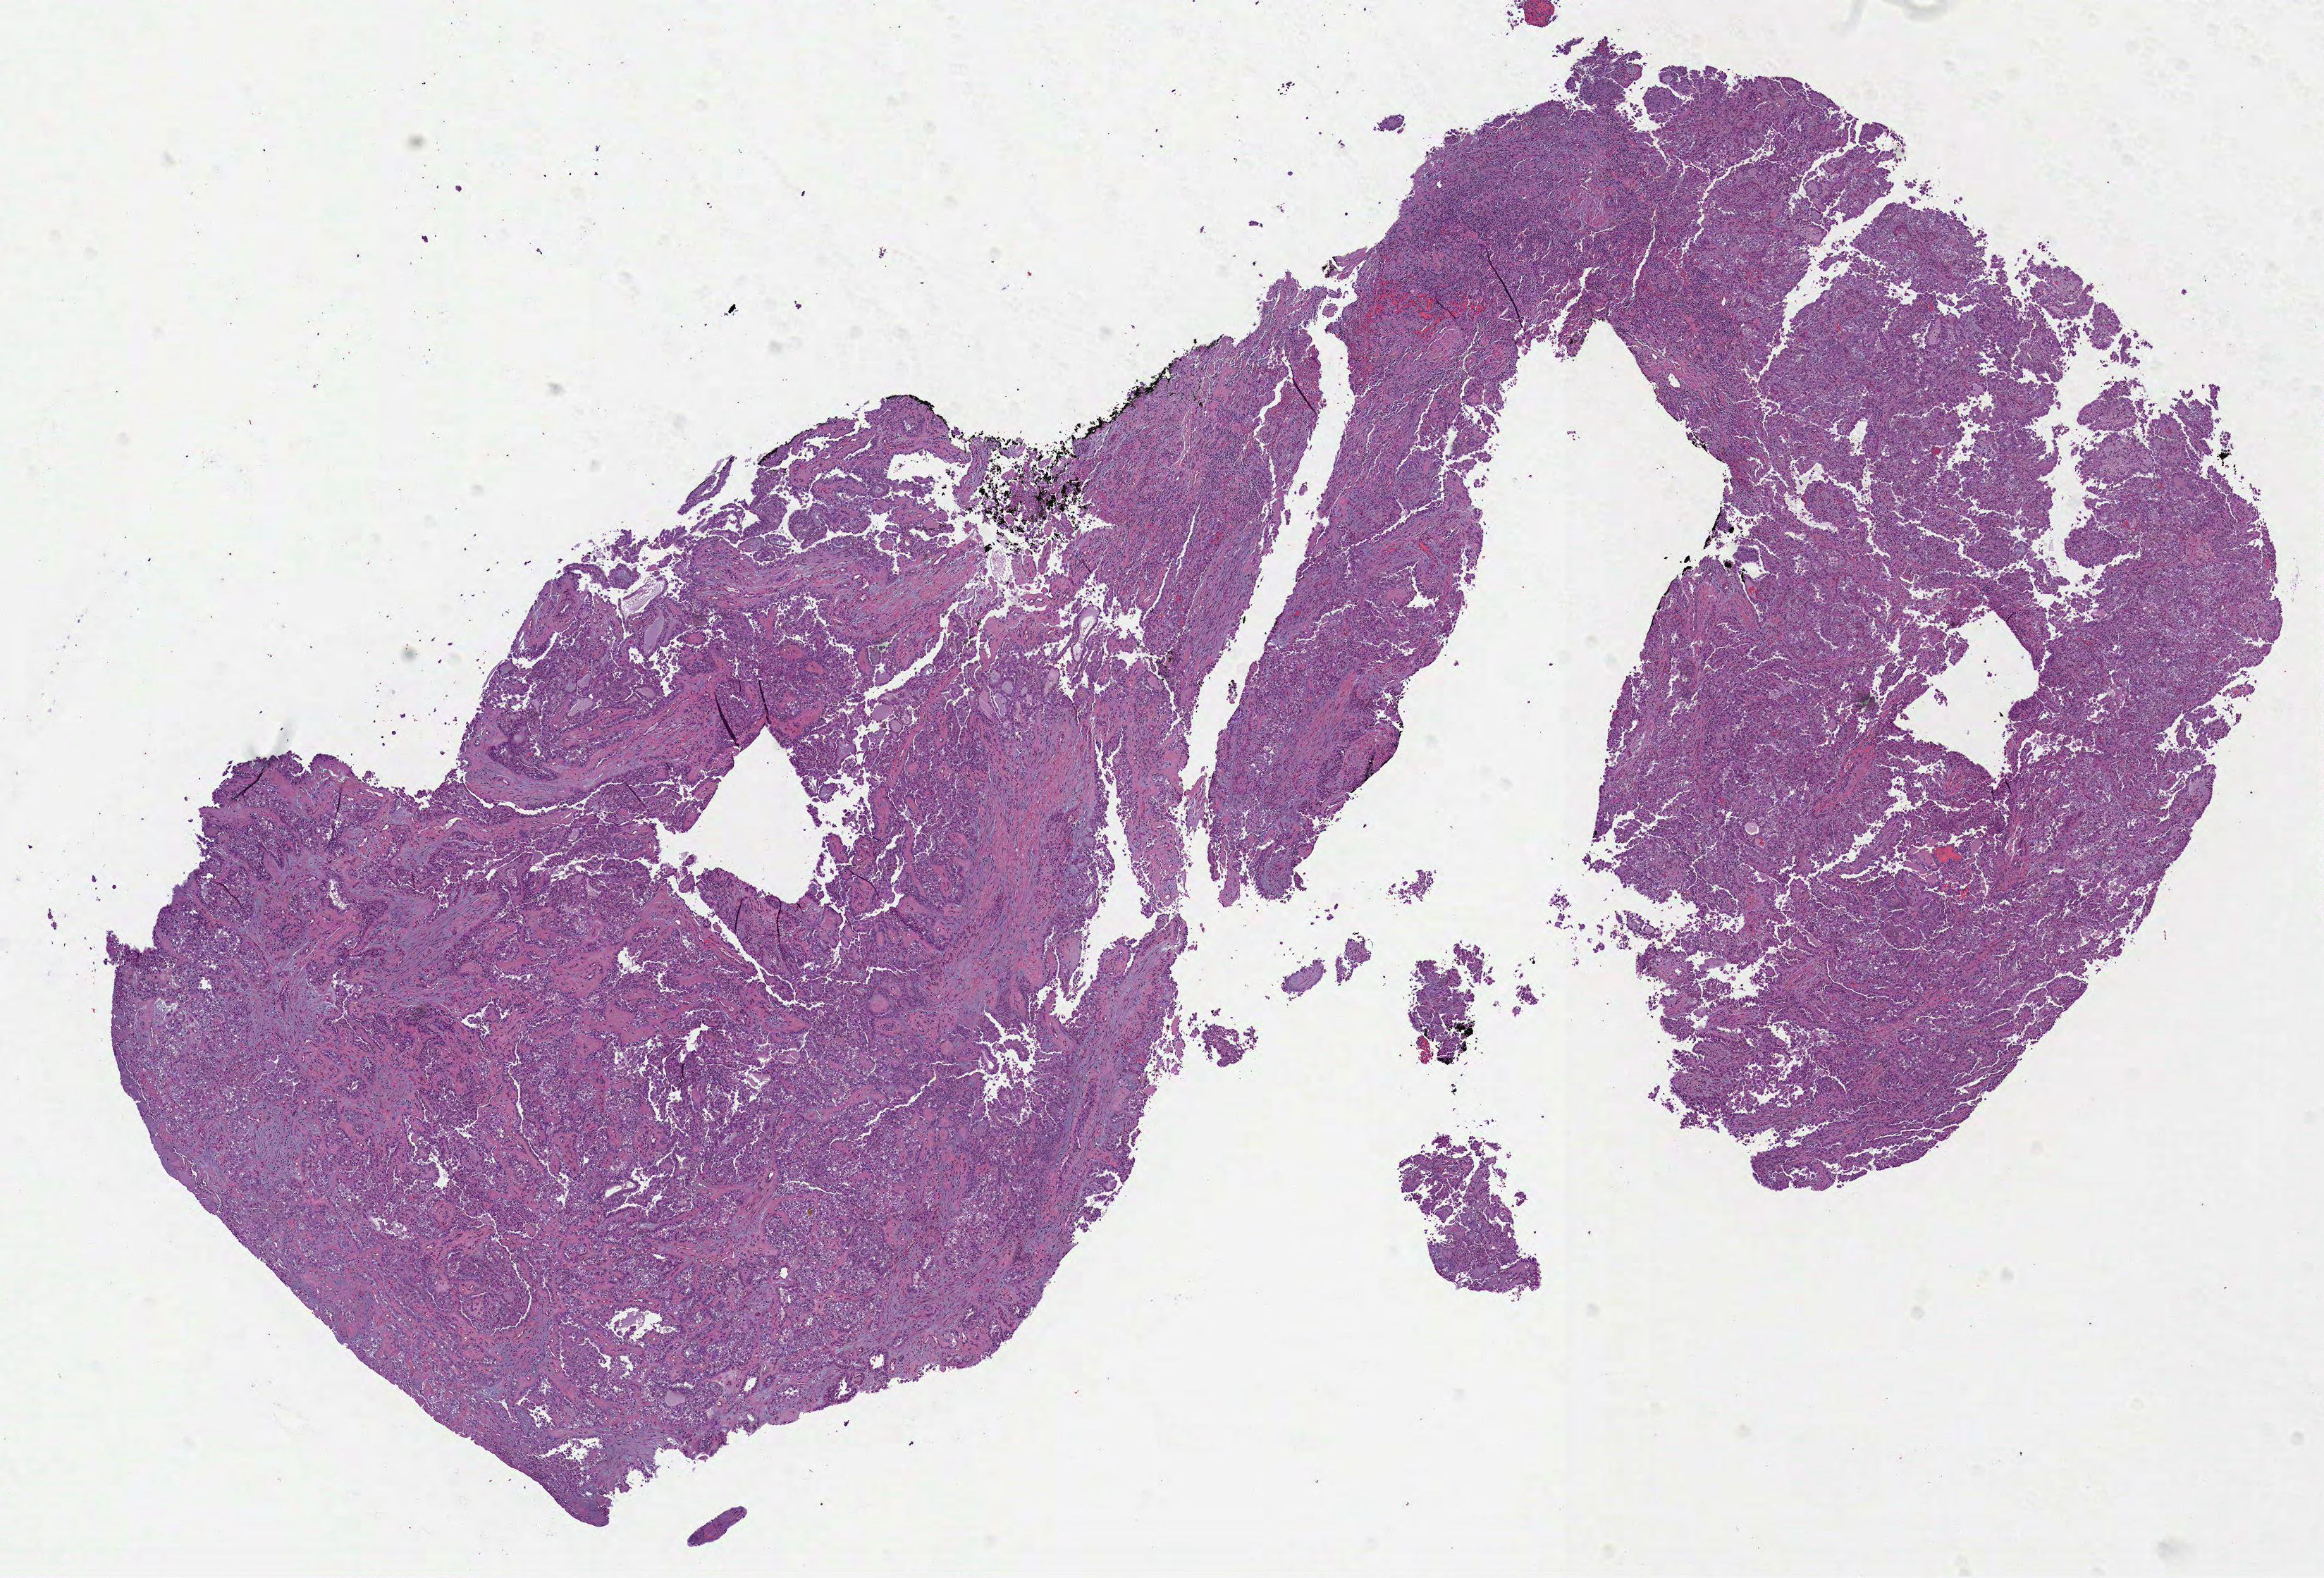
Digitized H&E tissue section (whole slide), a low-resolution overview of the entire scanned area, about 13.3 x 9.0 mm (from a 40x scan); formalin-fixed paraffin-embedded (FFPE) diagnostic section; sample: primary tumour, kidney. Female patient; age at initial diagnosis 35 years.
Lymph nodes positive (case pathology): 0 of 2 examined. AJCC pathologic stage: II. Diagnosis: Papillary adenocarcinoma, NOS.